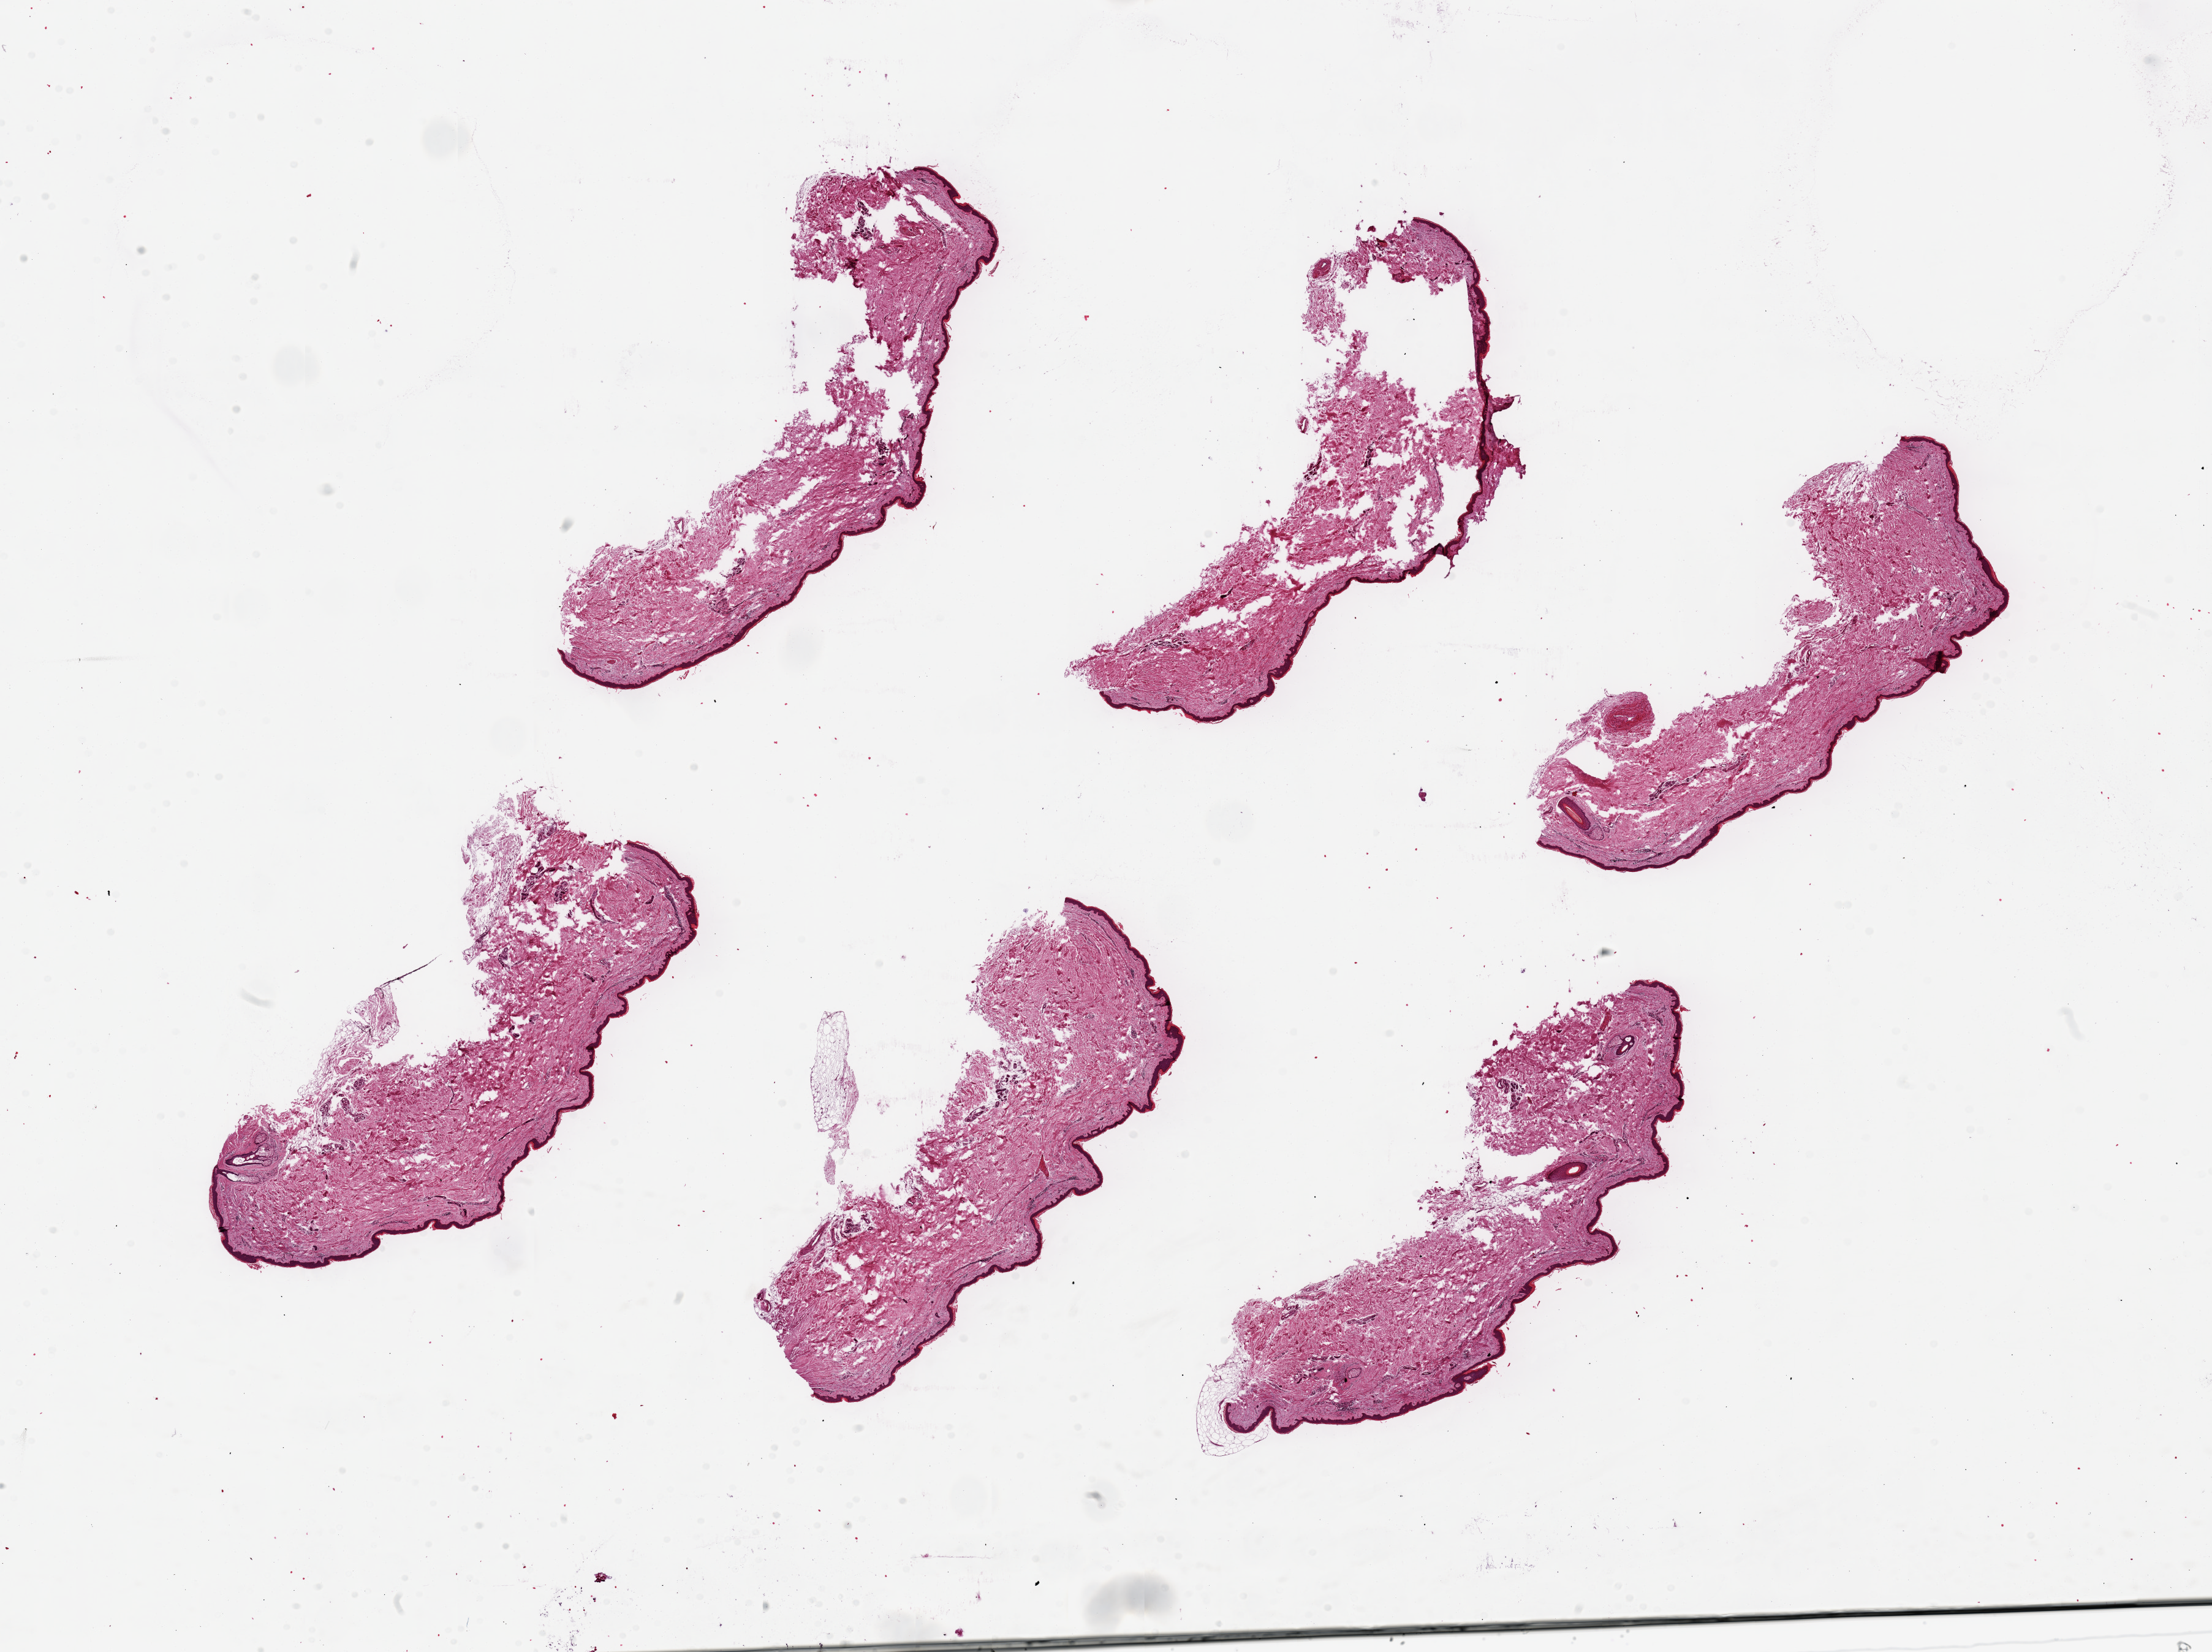
Haematoxylin and eosin whole-slide image — a low-resolution overview of the entire scanned area, about 28.5 x 21.3 mm (from a 20x scan); PAXgene-fixed, paraffin-embedded tissue; section of skin of lower leg (target tissue); tissue donor sample. Male donor.
Pathologist's review note for this sample: 6 pieces up to 8x2 mm; most subcutaneous adipose removed; considerable tissue fracture.